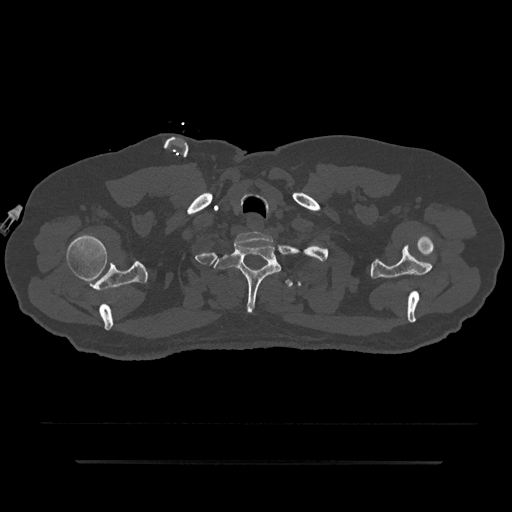
CT including the spine, one axial slice; position 738 of 797 along the scan axis; 120 kVp; bone window (W 1800 / L 400 HU); 512 × 512 image matrix, field of view 464 × 464 mm. Male patient, age 59 years. Case-level facts recorded for this patient, not image findings: primary cancer: bile ducts; vertebrae with lytic lesions (as recorded): T10.
Outlined on this slice (semi-automatically segmented with operator editing):
- T1 vertebra: box from (x=214, y=244) to (x=282, y=313) px
- T2 vertebra: (x=285, y=279)–(x=293, y=287)